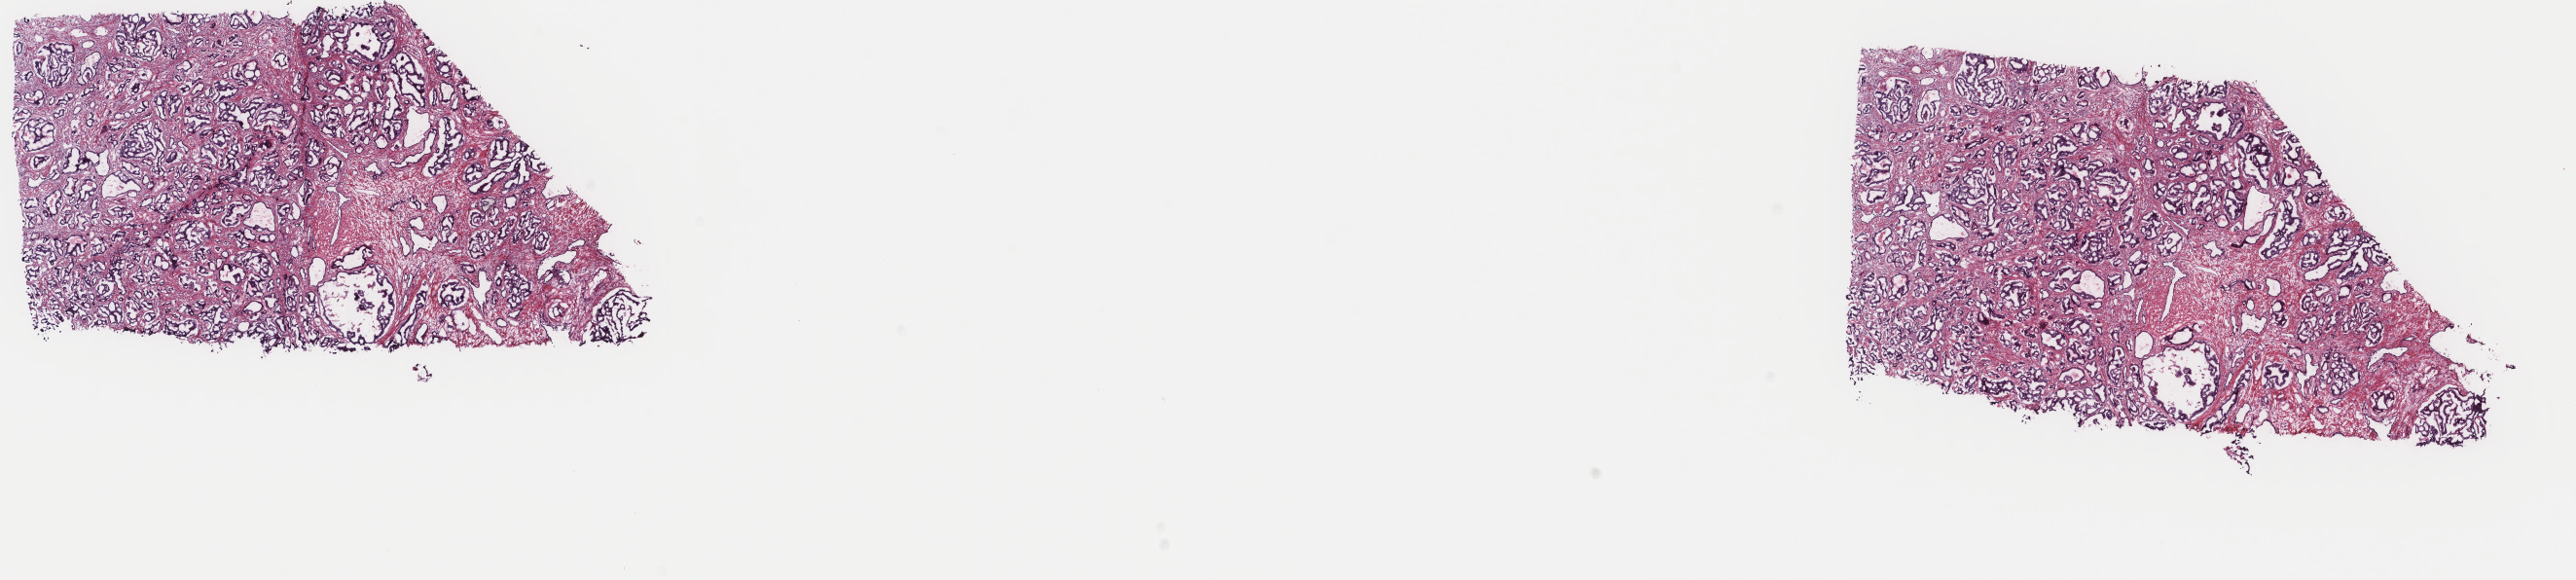
Digitized H&E tissue section (whole slide), shown as a low-resolution overview of the whole scanned area (about 21.0 x 4.7 mm, acquisition: 40x scan); frozen section from the top of the tissue portion; primary tumour sample from the prostate. Male patient; age at initial diagnosis 65 years. Gleason score: 7 (4+3). Pathologist review of this section (percent, as recorded): tumour cells 45%, tumour nuclei 80%, normal cells 0%, stromal cells 51%, necrosis 4%. Inflammatory infiltration, as recorded: lymphocyte infiltration 3%, monocyte infiltration 0%, neutrophil infiltration 2%.
* laterality: bilateral
* diagnosis: Adenocarcinoma, NOS (prostate gland)